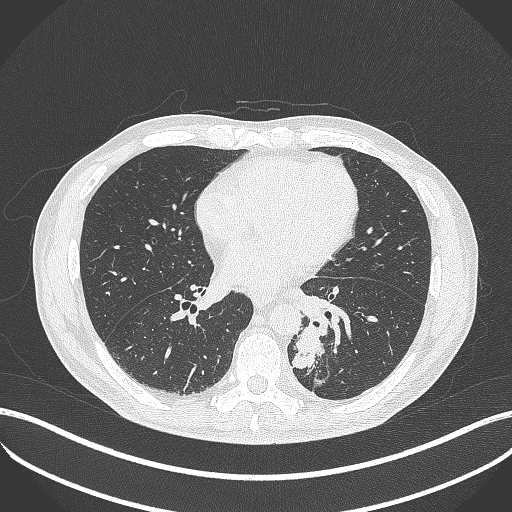
Chest CT, one axial slice; slice 170 of 451 in the series (ordered by position); reconstruction kernel B70f; lung window (W 1500 / L -600 HU); 1 mm slice thickness; 512 × 512 image matrix, field of view 400 × 400 mm. Male patient, age 72 years. Case-level facts recorded for this patient, not image findings: clinical TNM (as recorded): T2b N0 M1.
Structures marked on this image (rectangle marked by the reading radiologist):
- lung tumour (recorded histology: adenocarcinoma): bounding box <290,319,326,374> (left, top, right, bottom; pixels)